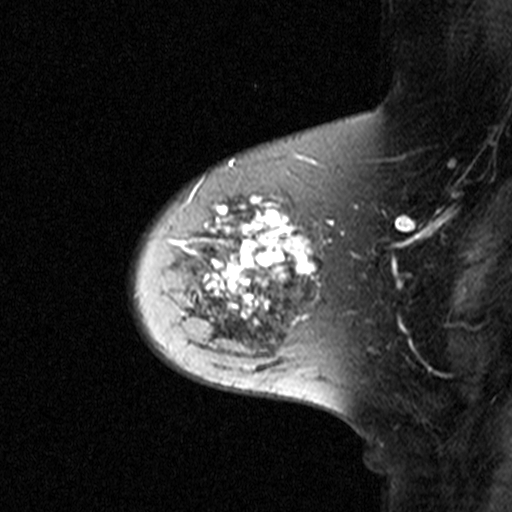
Breast MRI (dynamic contrast-enhanced), one sagittal slice; slice 32 of 44 in the series (ordered by position); dynamic contrast-enhanced study with each time point stored as its own series, time point 2 of 3 at this slice position (early post-contrast, ordered by acquisition time); 1.5 T; TE 4.5 ms, TR 11 ms; 3 mm slice thickness; 512 × 512 image matrix, field of view 200 × 200 mm. Patient: female, 65 years. From the clinical record (not read from this slice): setting: breast cancer imaged before/during neoadjuvant chemotherapy; receptor status: HER2-positive.
Outlined on this slice (semi-automatic segmentation, software-assisted and operator-edited):
- analysis volume of interest (the breast-tissue region the enhancement analysis was run in; not a lesion): bounding box (x1, y1, x2, y2) in pixels: (160, 172, 329, 345)
- tumour enhancement mask (voxels above the 90 % enhancement threshold inside the analysis volume of interest): (183, 196, 316, 326)